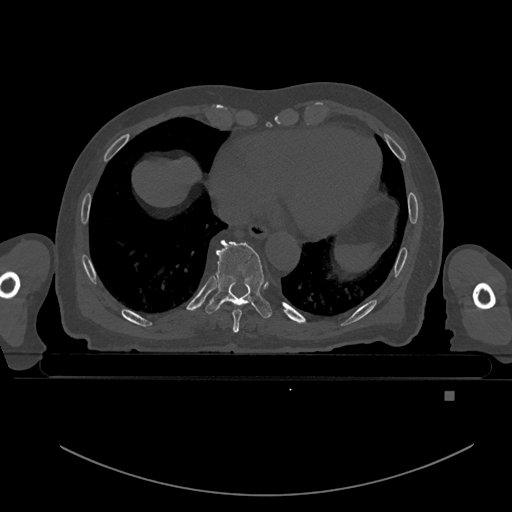
CT including the spine, one axial slice. Slice 160 of 969 in the series (ordered by position). Bone window (W 1800 / L 400 HU). 512 × 512 image matrix, field of view 456 × 456 mm. Male patient, age 82 years. From the clinical record (not read from this slice): primary cancer: prostate.
Structures marked on this image (semi-automatic segmentation, software-assisted and operator-edited):
- T8 vertebra: bounding box (x1, y1, x2, y2) in pixels: (232, 298, 242, 333)
- T9 vertebra: (205, 240, 272, 319)